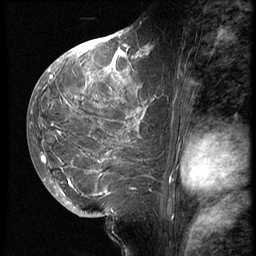
Breast MRI (dynamic contrast-enhanced), one sagittal slice; 3 images stored at this slice position (order not interpretable as contrast timing); 1.5 T; TE 4.2 ms, TR 9 ms; 256 × 256 image matrix, field of view 180 × 180 mm. Patient: female, 28 years. Case-level facts recorded for this patient, not image findings: setting: breast cancer imaged before/during neoadjuvant chemotherapy.
Annotated regions visible in this slice (semi-automatic segmentation, software-assisted and operator-edited):
- analysis volume of interest (the breast-tissue region the enhancement analysis was run in; not a lesion): box from (x=42, y=45) to (x=164, y=207) px
- tumour enhancement mask (voxels above the 140 % enhancement threshold inside the analysis volume of interest): (x=42, y=46)–(x=148, y=195)